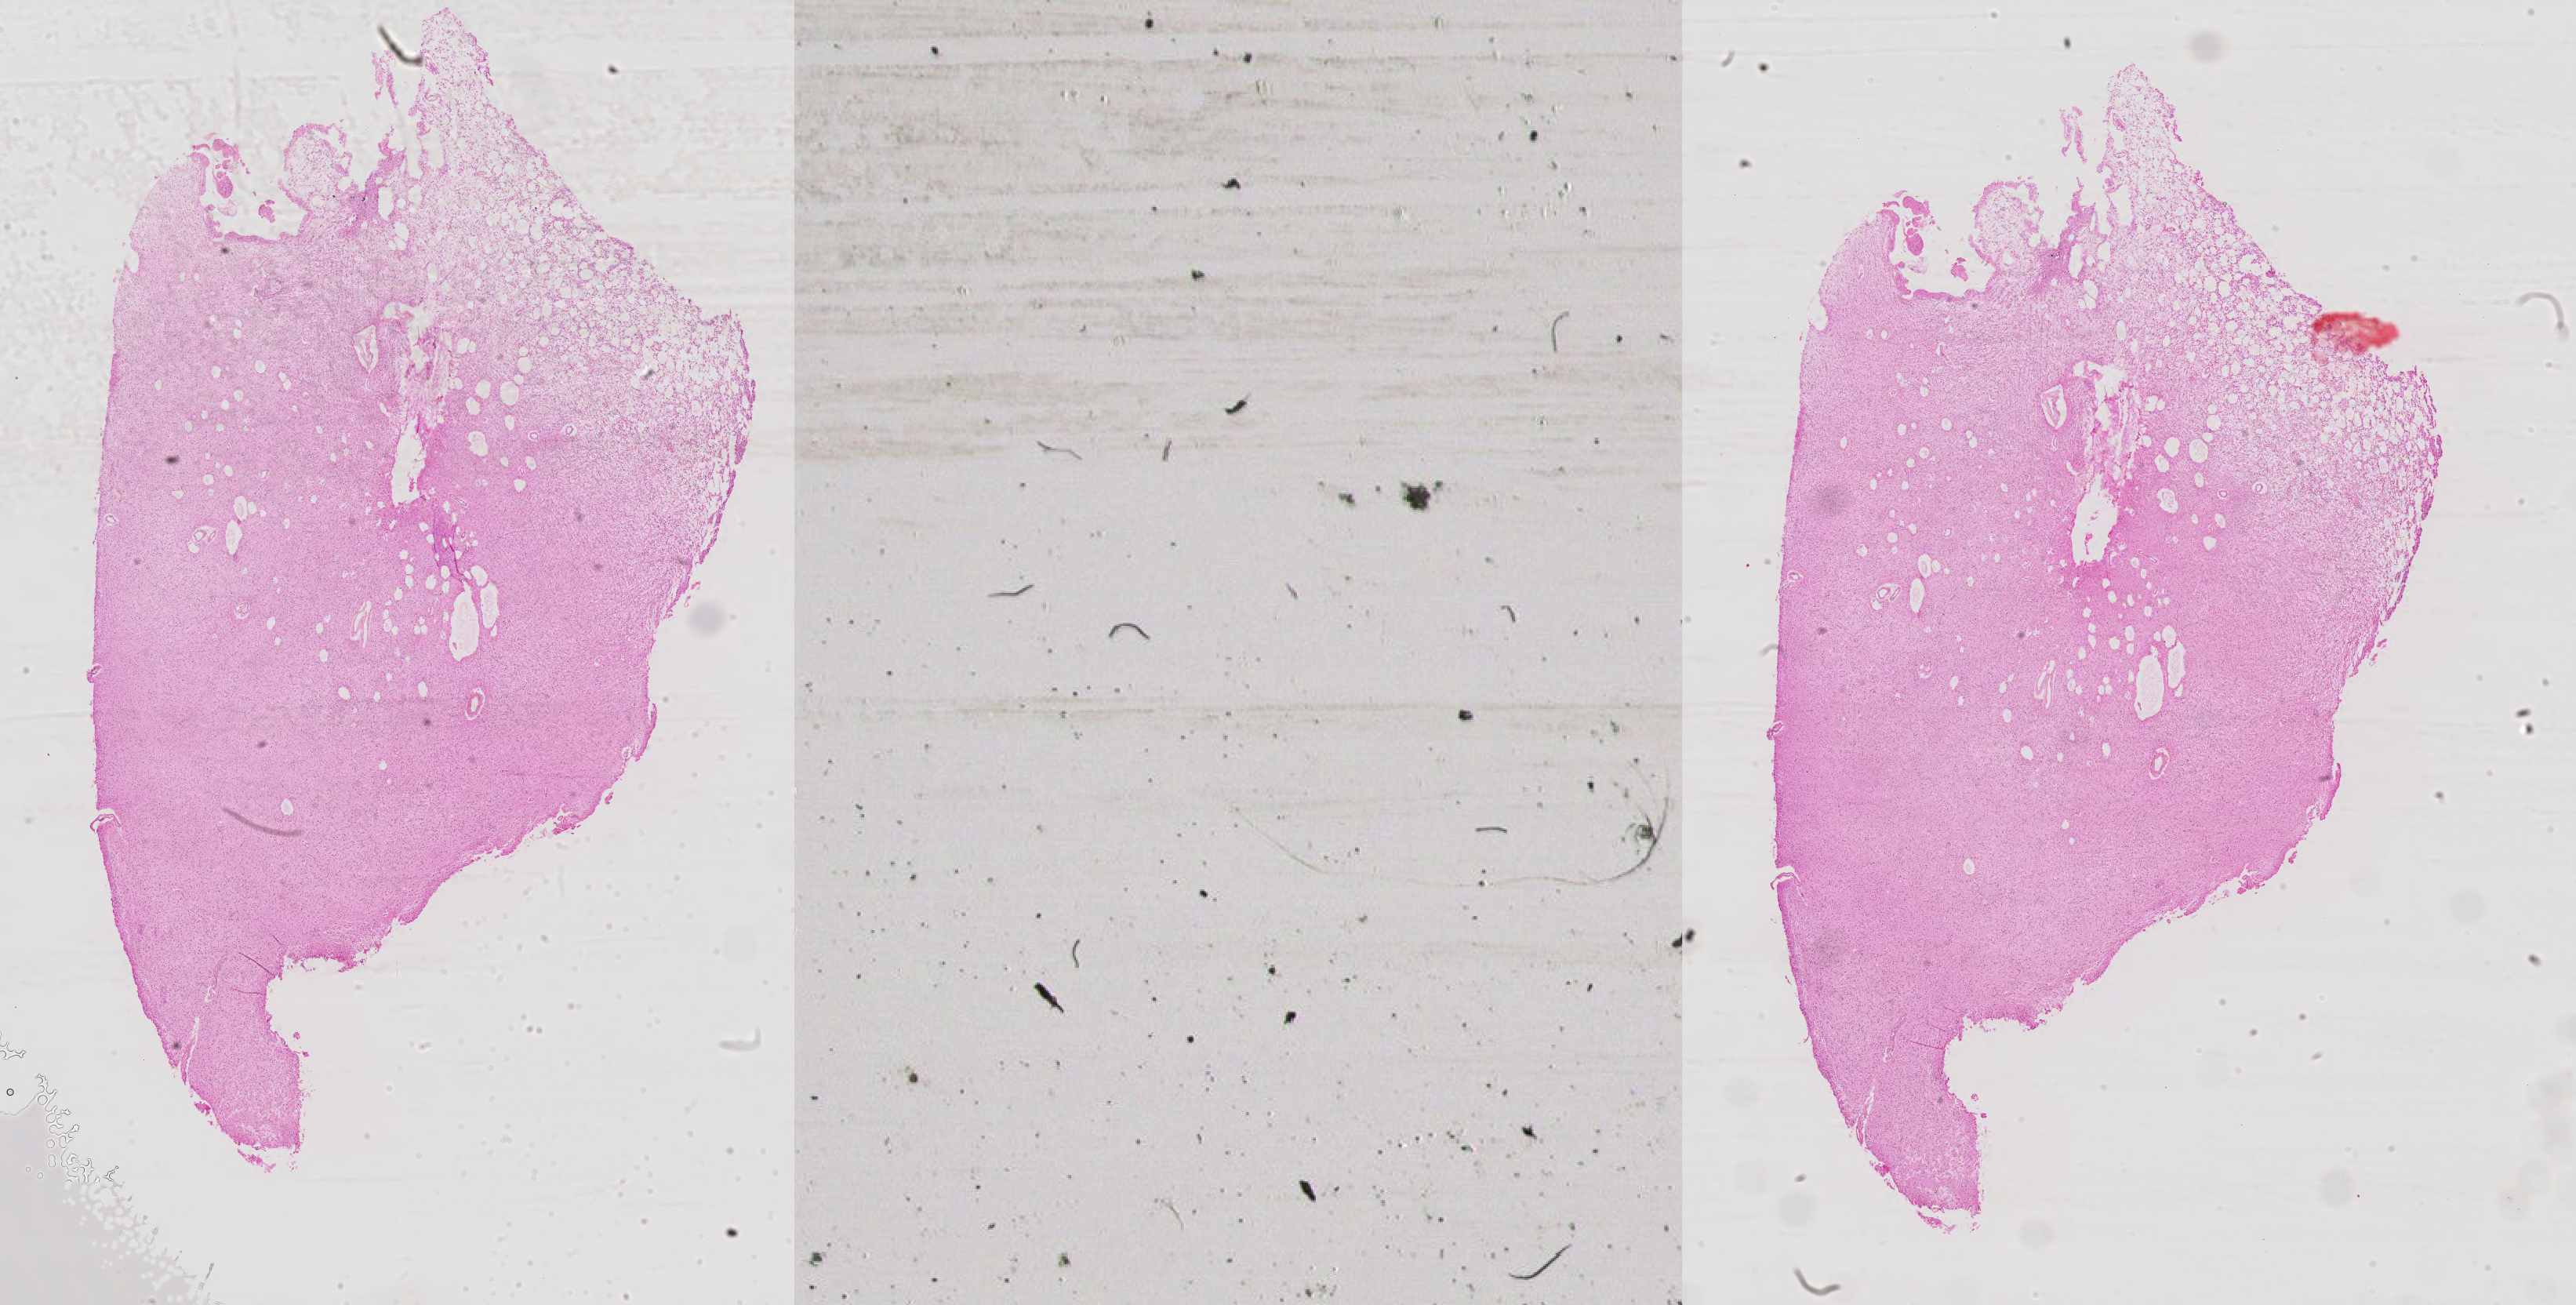
Hematoxylin and eosin (H&E) stained whole-slide image, a low-resolution overview of the entire scanned area, about 26.3 x 13.3 mm (acquisition: 40x scan). Formalin-fixed paraffin-embedded (FFPE) diagnostic section. Brain, primary tumour sample. Female, age 31 years at initial diagnosis. Histologic grade: G2 (moderately differentiated).
Laterality: right. Diagnosis: Astrocytoma, NOS (cerebrum).